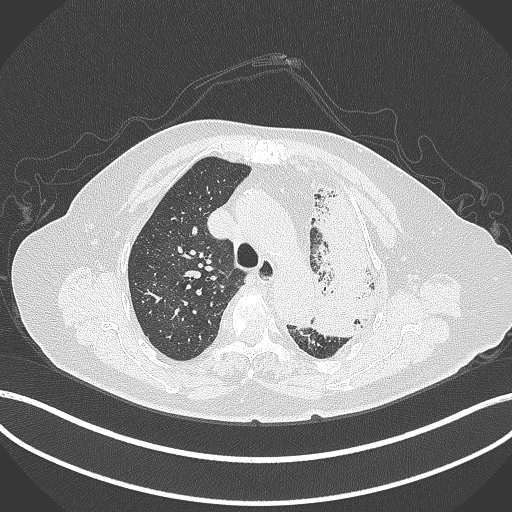
Chest CT, one axial slice. Slice 290 of 399 in the series (ordered by position). 120 kVp. Lung window (W 1500 / L -600 HU). 1 mm slice thickness. 512 × 512 image matrix, field of view 400 × 400 mm. Female patient, age 75 years. Case-level facts recorded for this patient, not image findings: clinical TNM (as recorded): T3 N3 M1.
Annotated regions visible in this slice (bounding box drawn by a radiologist):
- lung tumour (recorded histology: adenocarcinoma): bounding box [x1, y1, x2, y2] px = [301, 182, 383, 339]